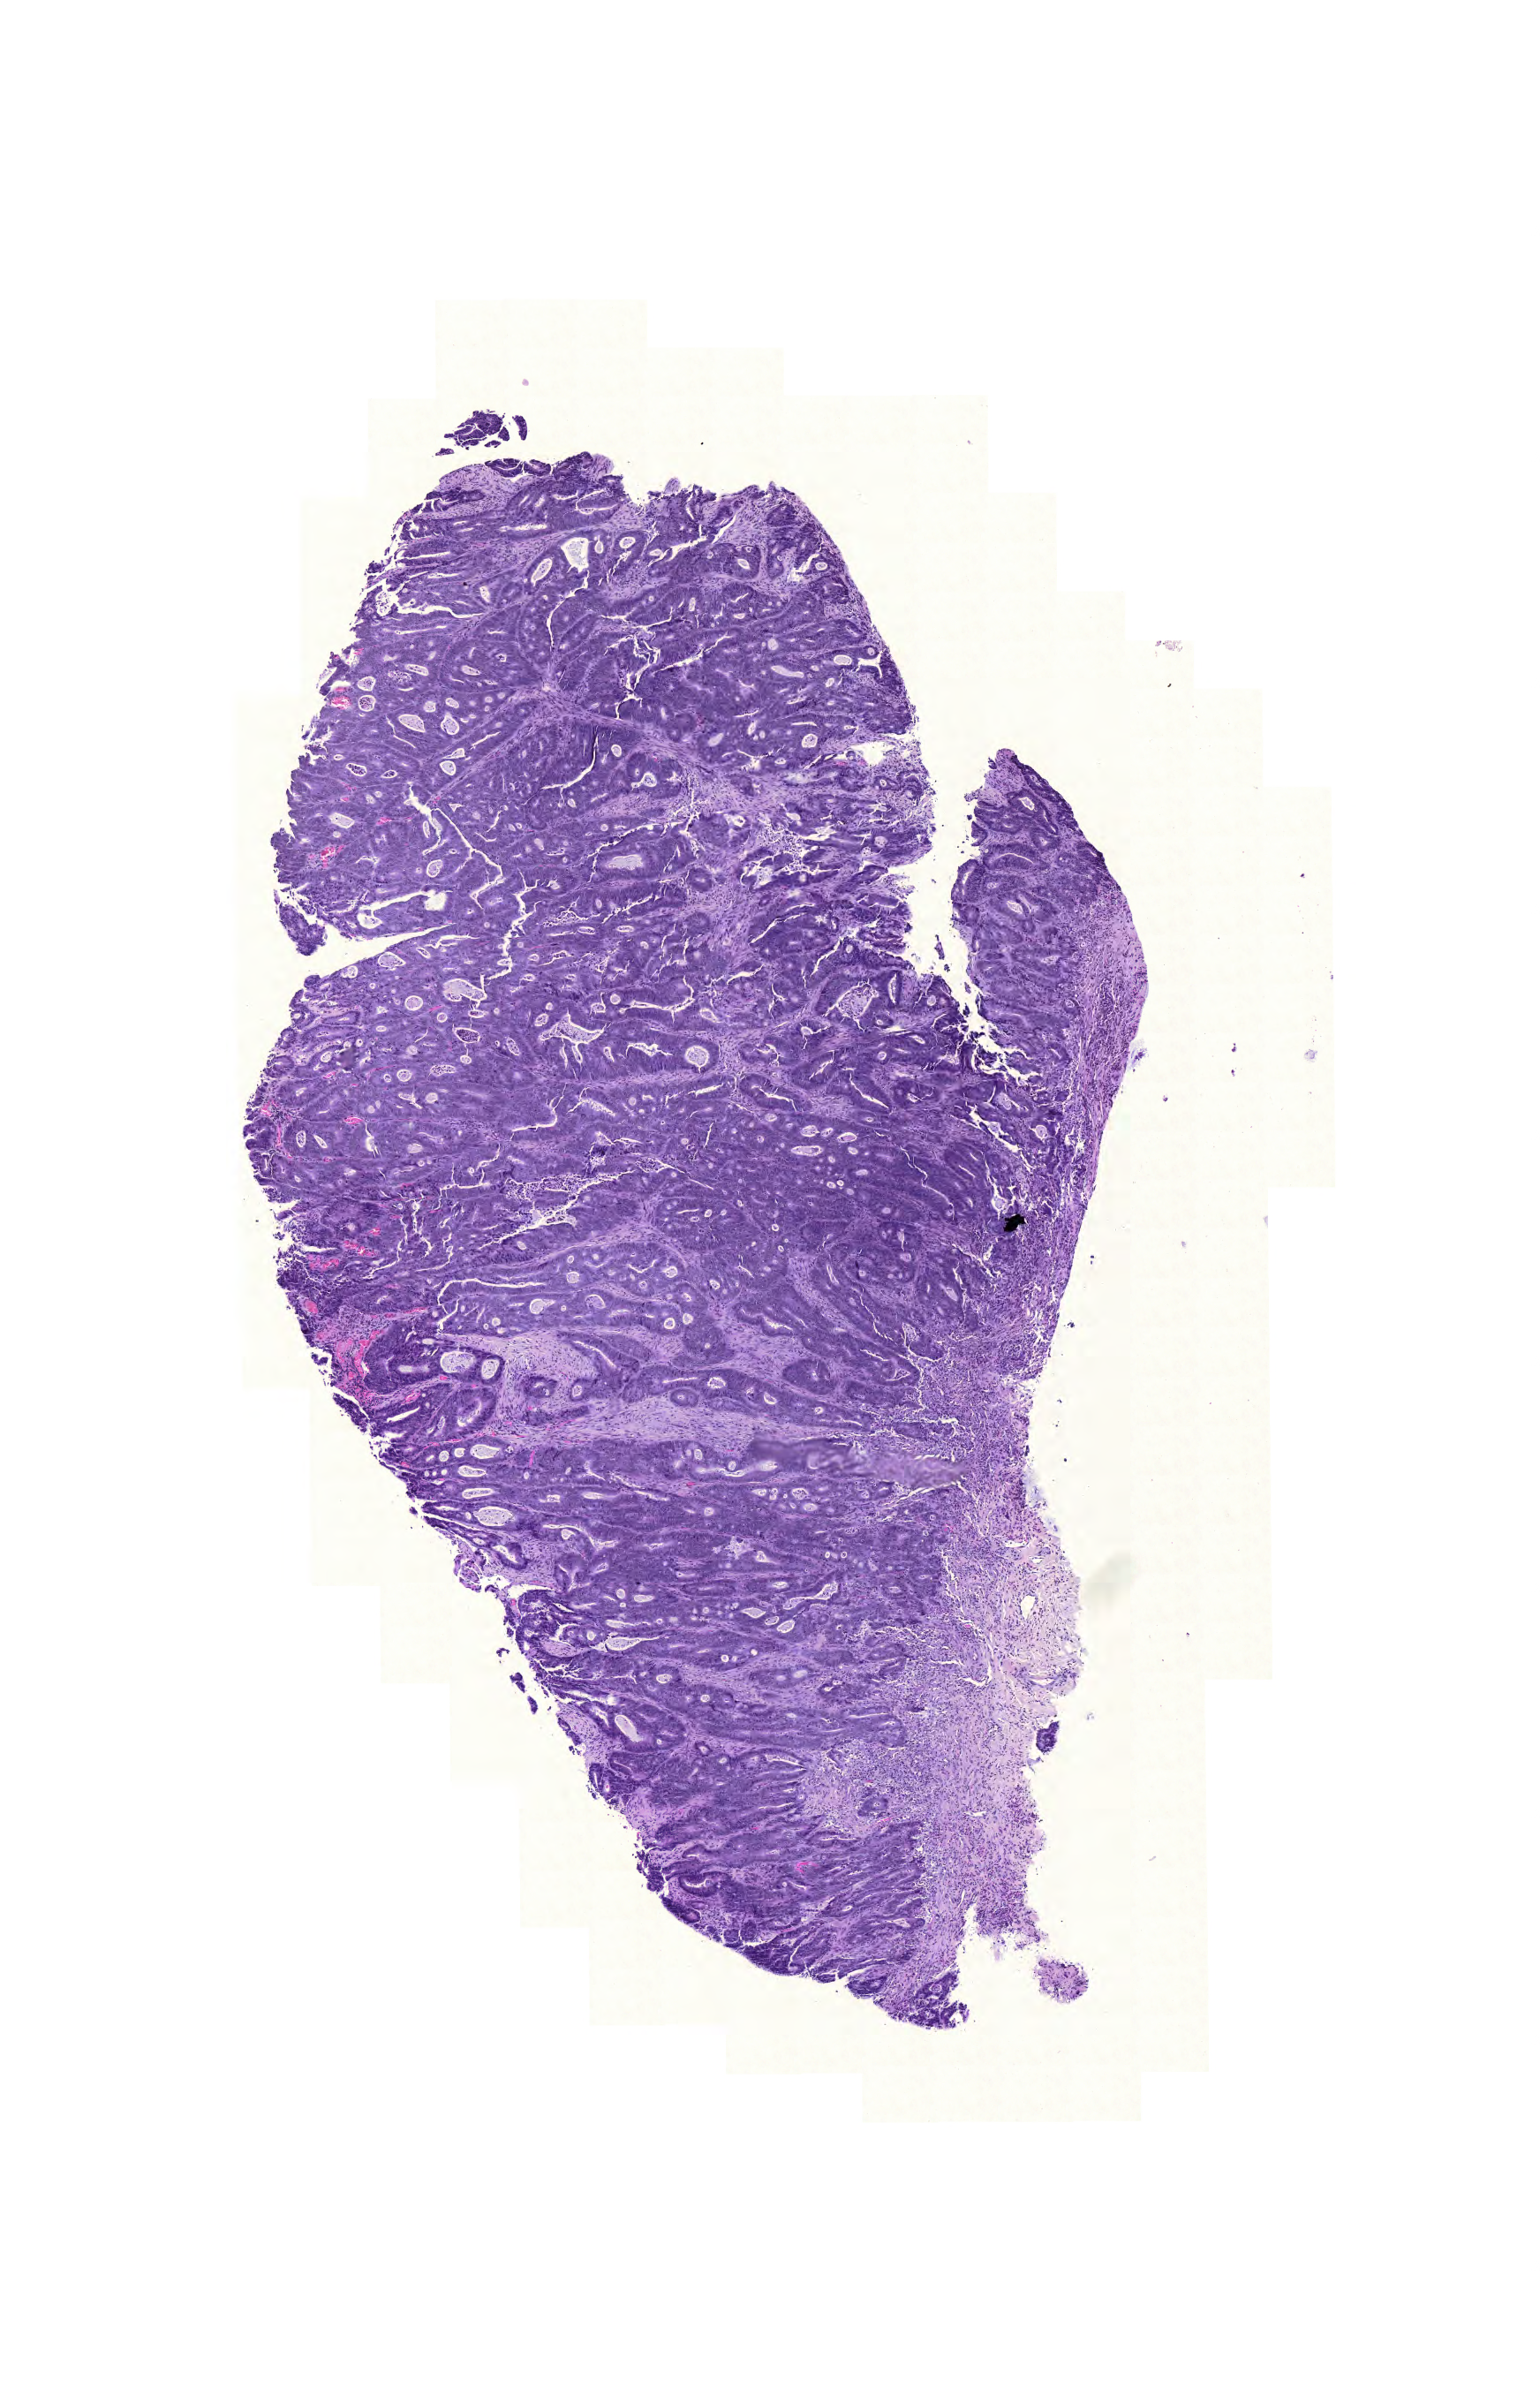
Whole-slide histology image, Hematoxylin and eosin (H&E) stained — a low-resolution overview of the entire scanned area, about 6.5 x 10.1 mm (slide scanned at 20x), formalin-fixed paraffin-embedded (FFPE) diagnostic section, sample: primary tumour, rectum. Male patient; age at initial diagnosis 64 years.
Pathologic diagnosis: Adenocarcinoma, NOS. Lymph nodes positive (case pathology): 0 of 15 examined. AJCC pathologic stage: I (6th edition).